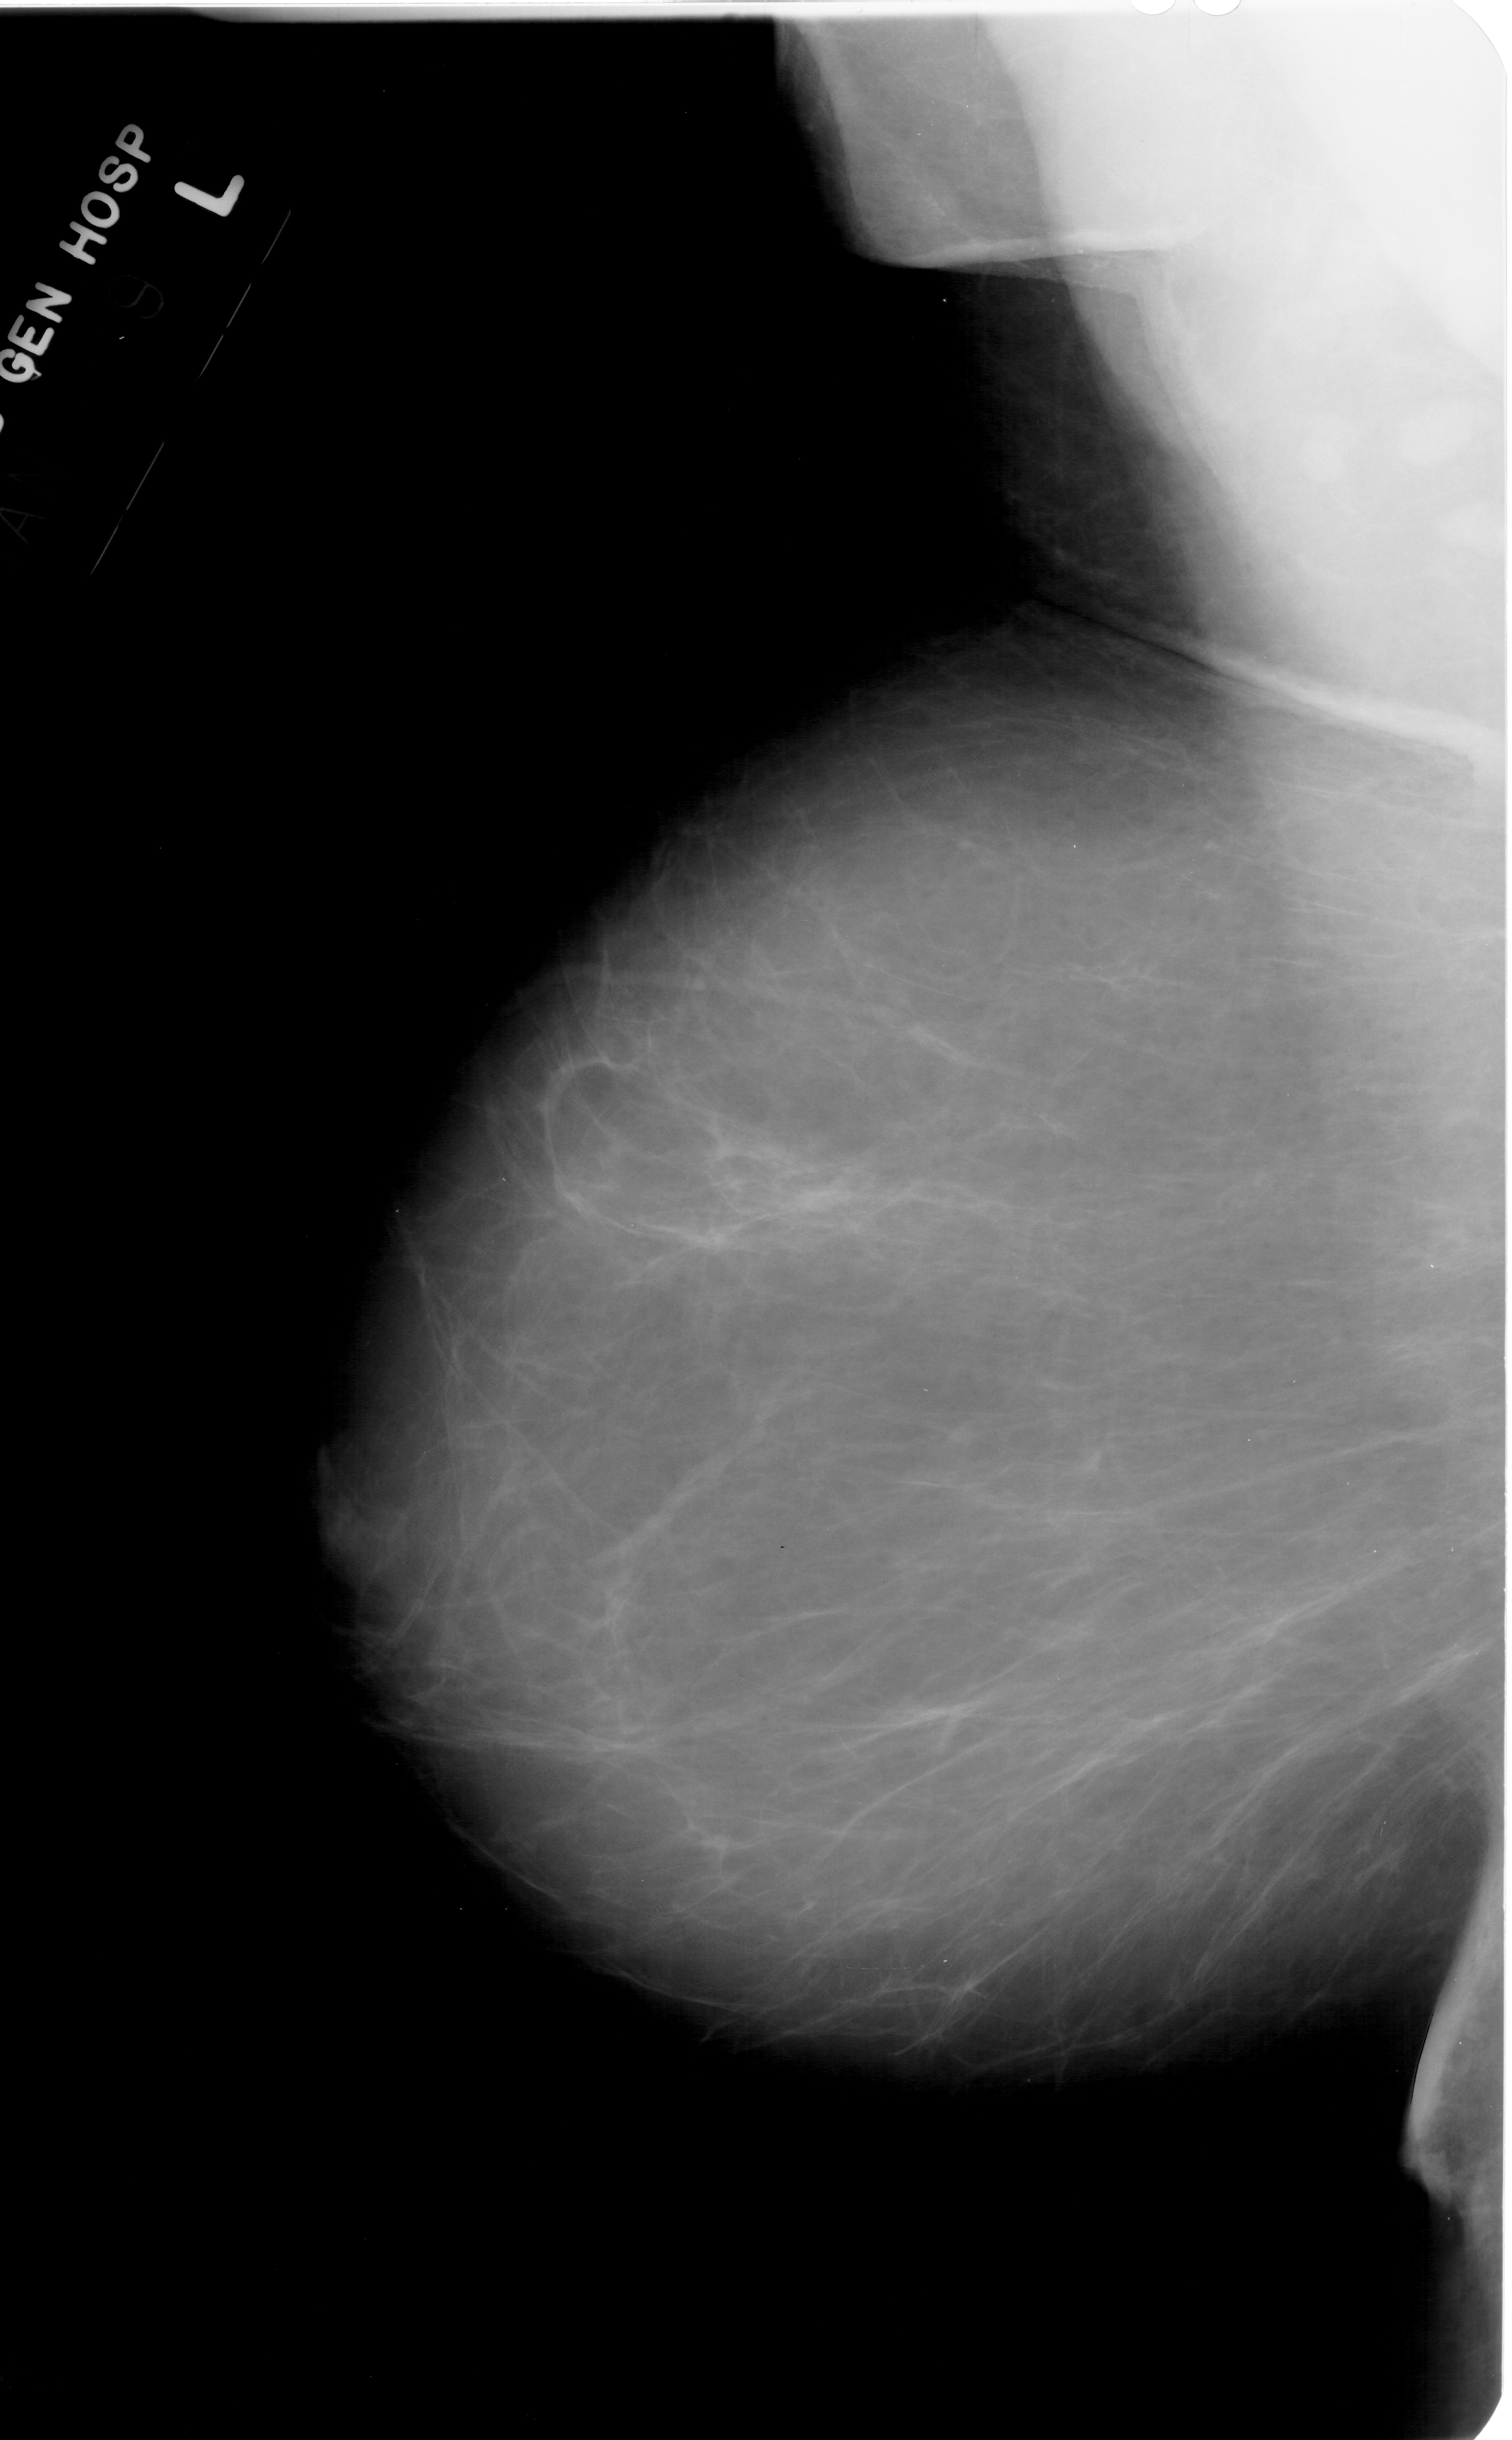
Scanned film-screen mammogram. Left breast. MLO view. BI-RADS breast density category 1 (scale 1–4). 1512 × 2440 image matrix.
Expert-marked regions of interest on this film, with their recorded descriptors:
- mass, shape irregular, margins ill defined; BI-RADS assessment category 2; pathology (as recorded): benign: box from (x=306, y=1443) to (x=393, y=1576) px